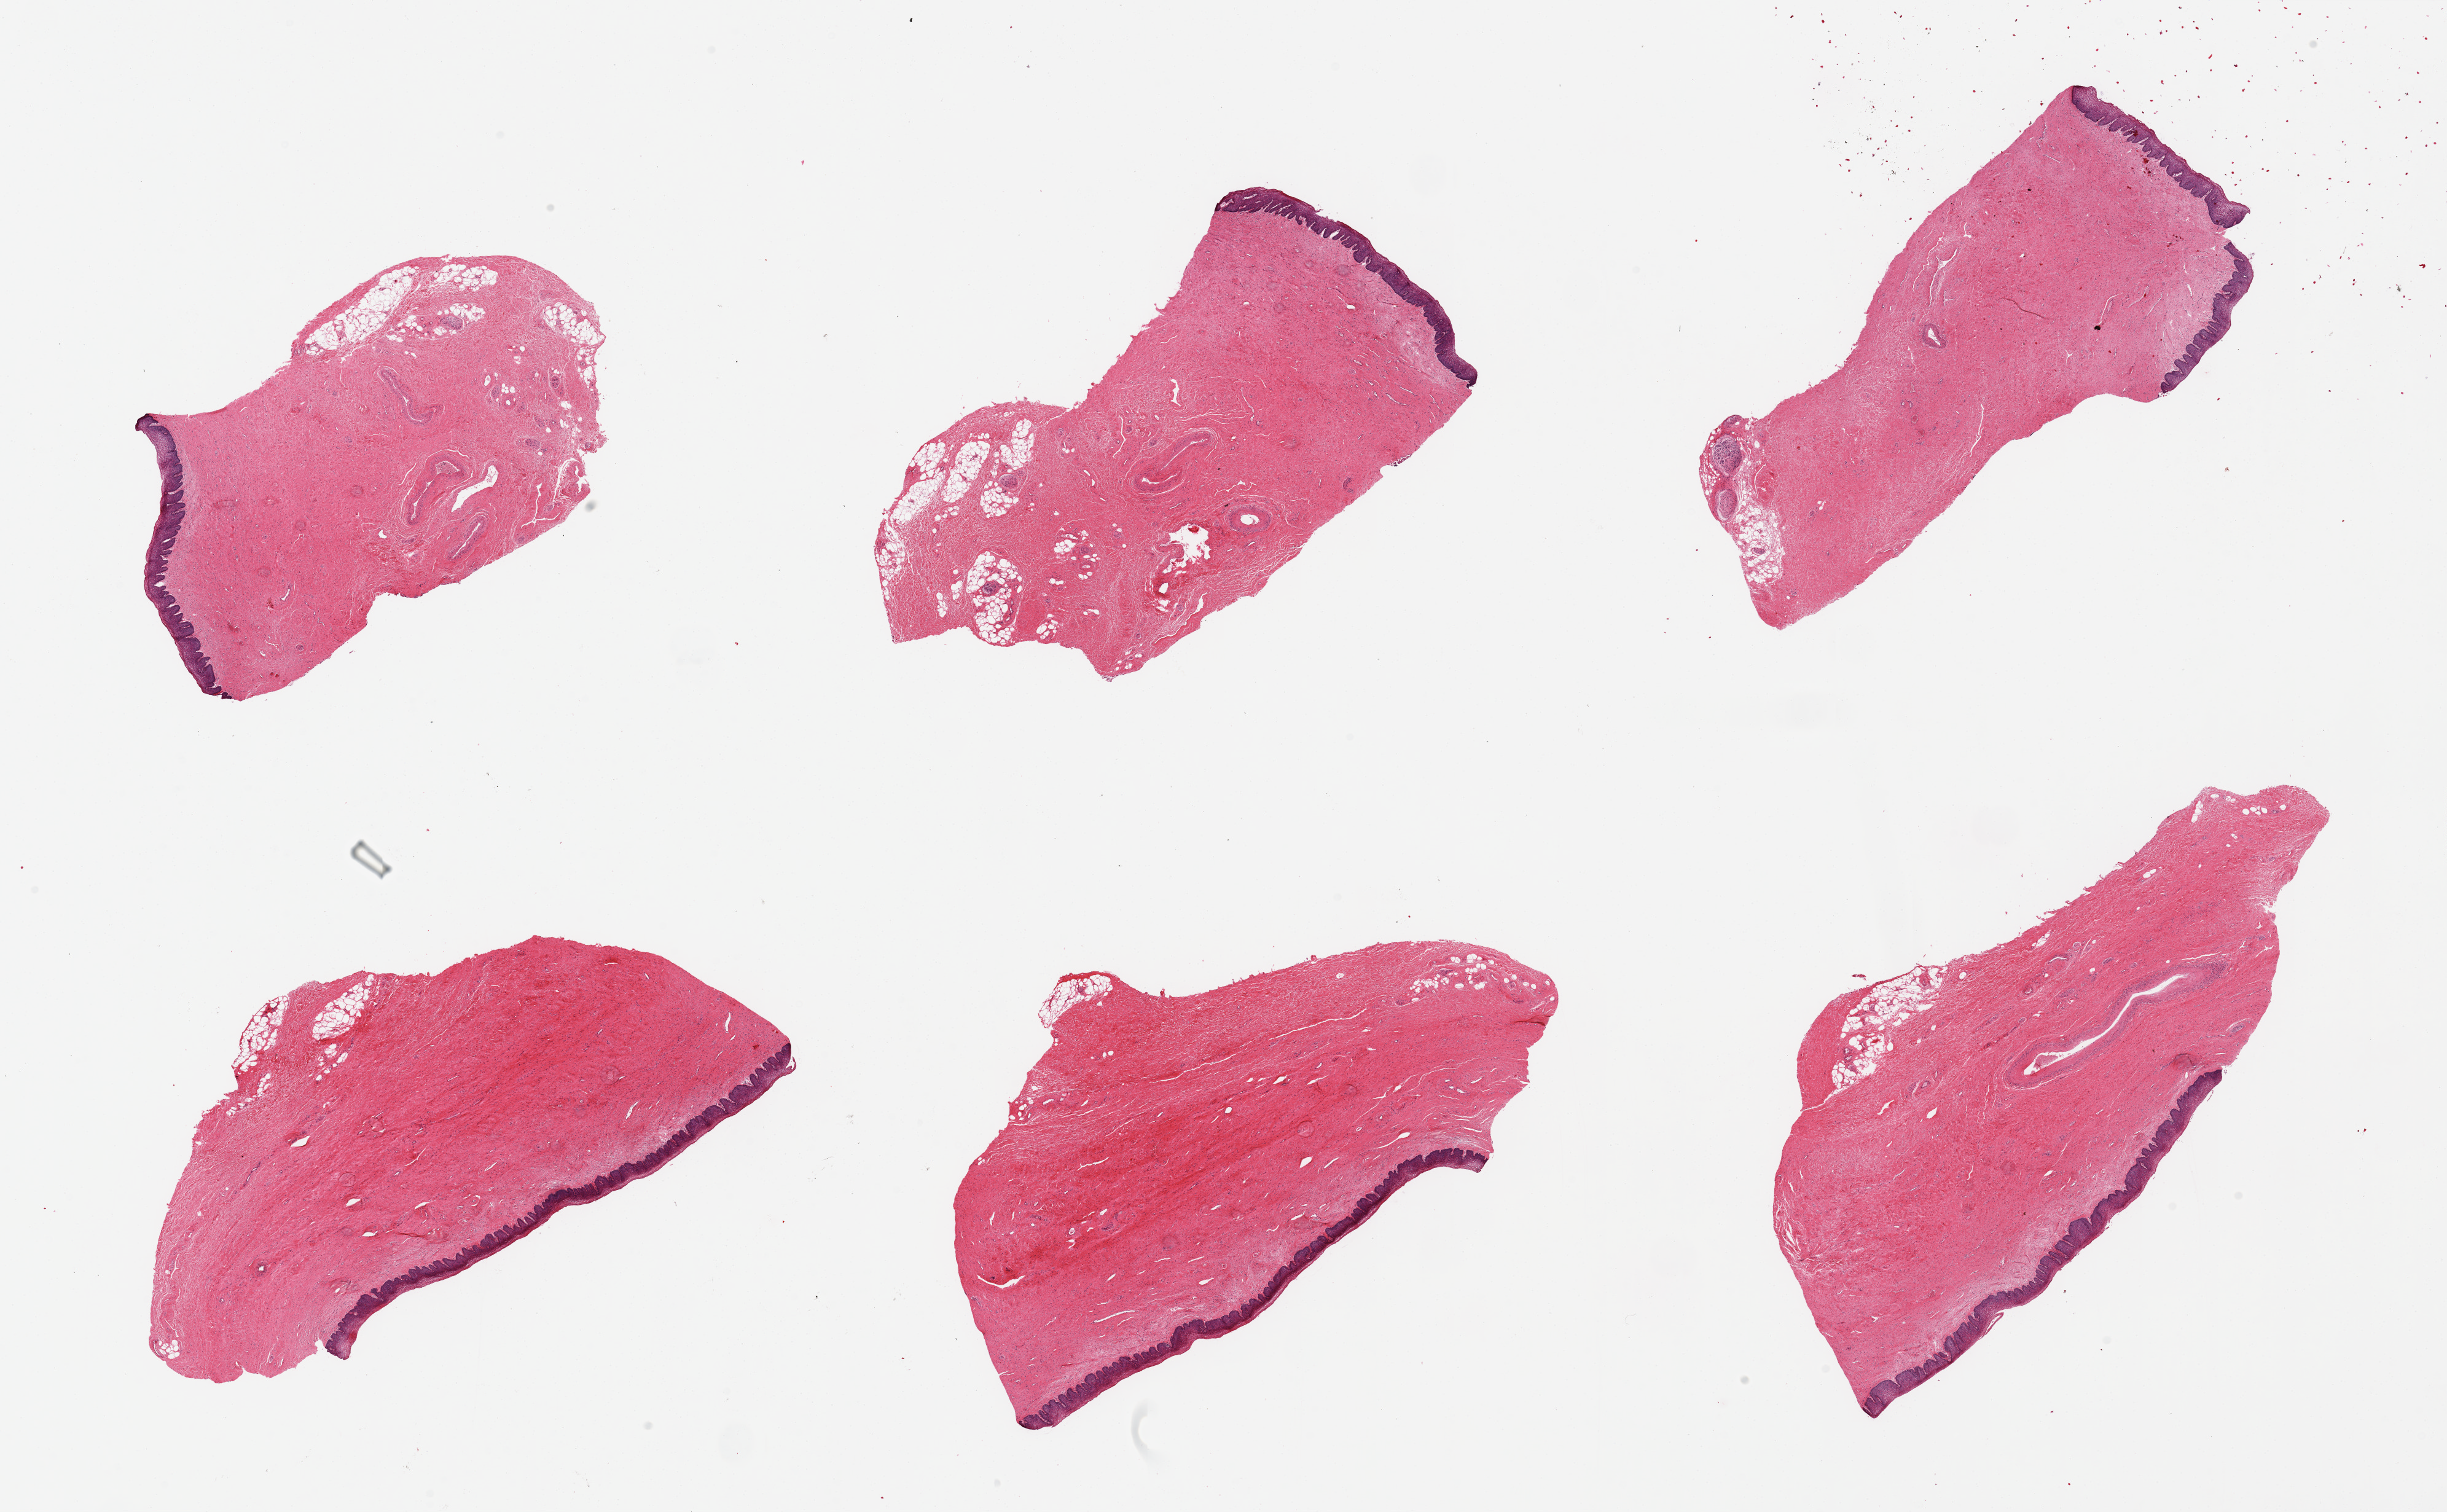
Digitized haematoxylin and eosin-stained section, brightfield — a low-resolution overview of the entire scanned area, about 31.5 x 19.5 mm (from a 20x scan). PAXgene-fixed, paraffin-embedded tissue. Section of vagina (target tissue). Tissue donor sample. Donor: female.
• review note (as recorded): 6 pieces; included 5-10% internal/external fat